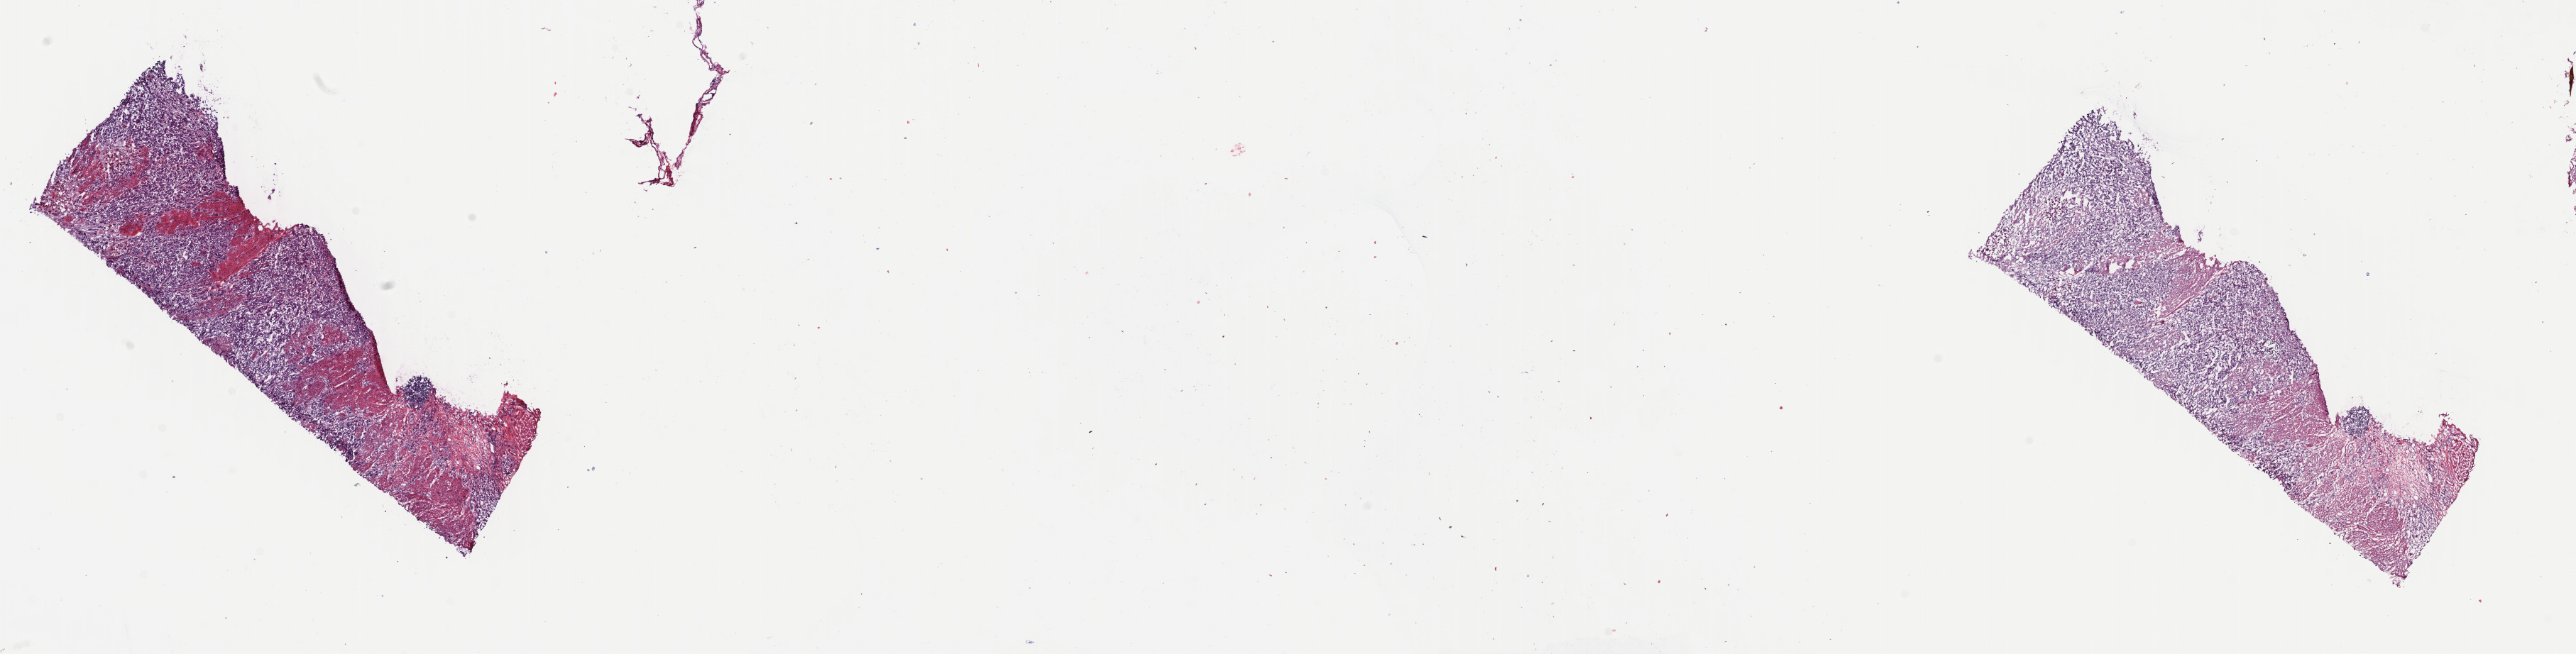
Hematoxylin and eosin (H&E) stained whole-slide image, whole scanned area (about 28.6 x 7.3 mm, from a 40x scan) shown as a low-resolution overview; frozen section from the top of the tissue portion; sample: primary tumour, bladder. Female patient; age at initial diagnosis 80 years. Histologic grade: high grade. Pathologist review of this section (percent, as recorded): tumour cells 70%, tumour nuclei 70%, normal cells 0%, stromal cells 30%, necrosis 0%. Inflammatory infiltration, as recorded: lymphocyte infiltration 5%, monocyte infiltration 0%, neutrophil infiltration 0%.
* pathologic diagnosis: Transitional cell carcinoma
* AJCC pathologic stage: IV (7th edition)
* lymph nodes positive (case pathology): 11 of 11 examined